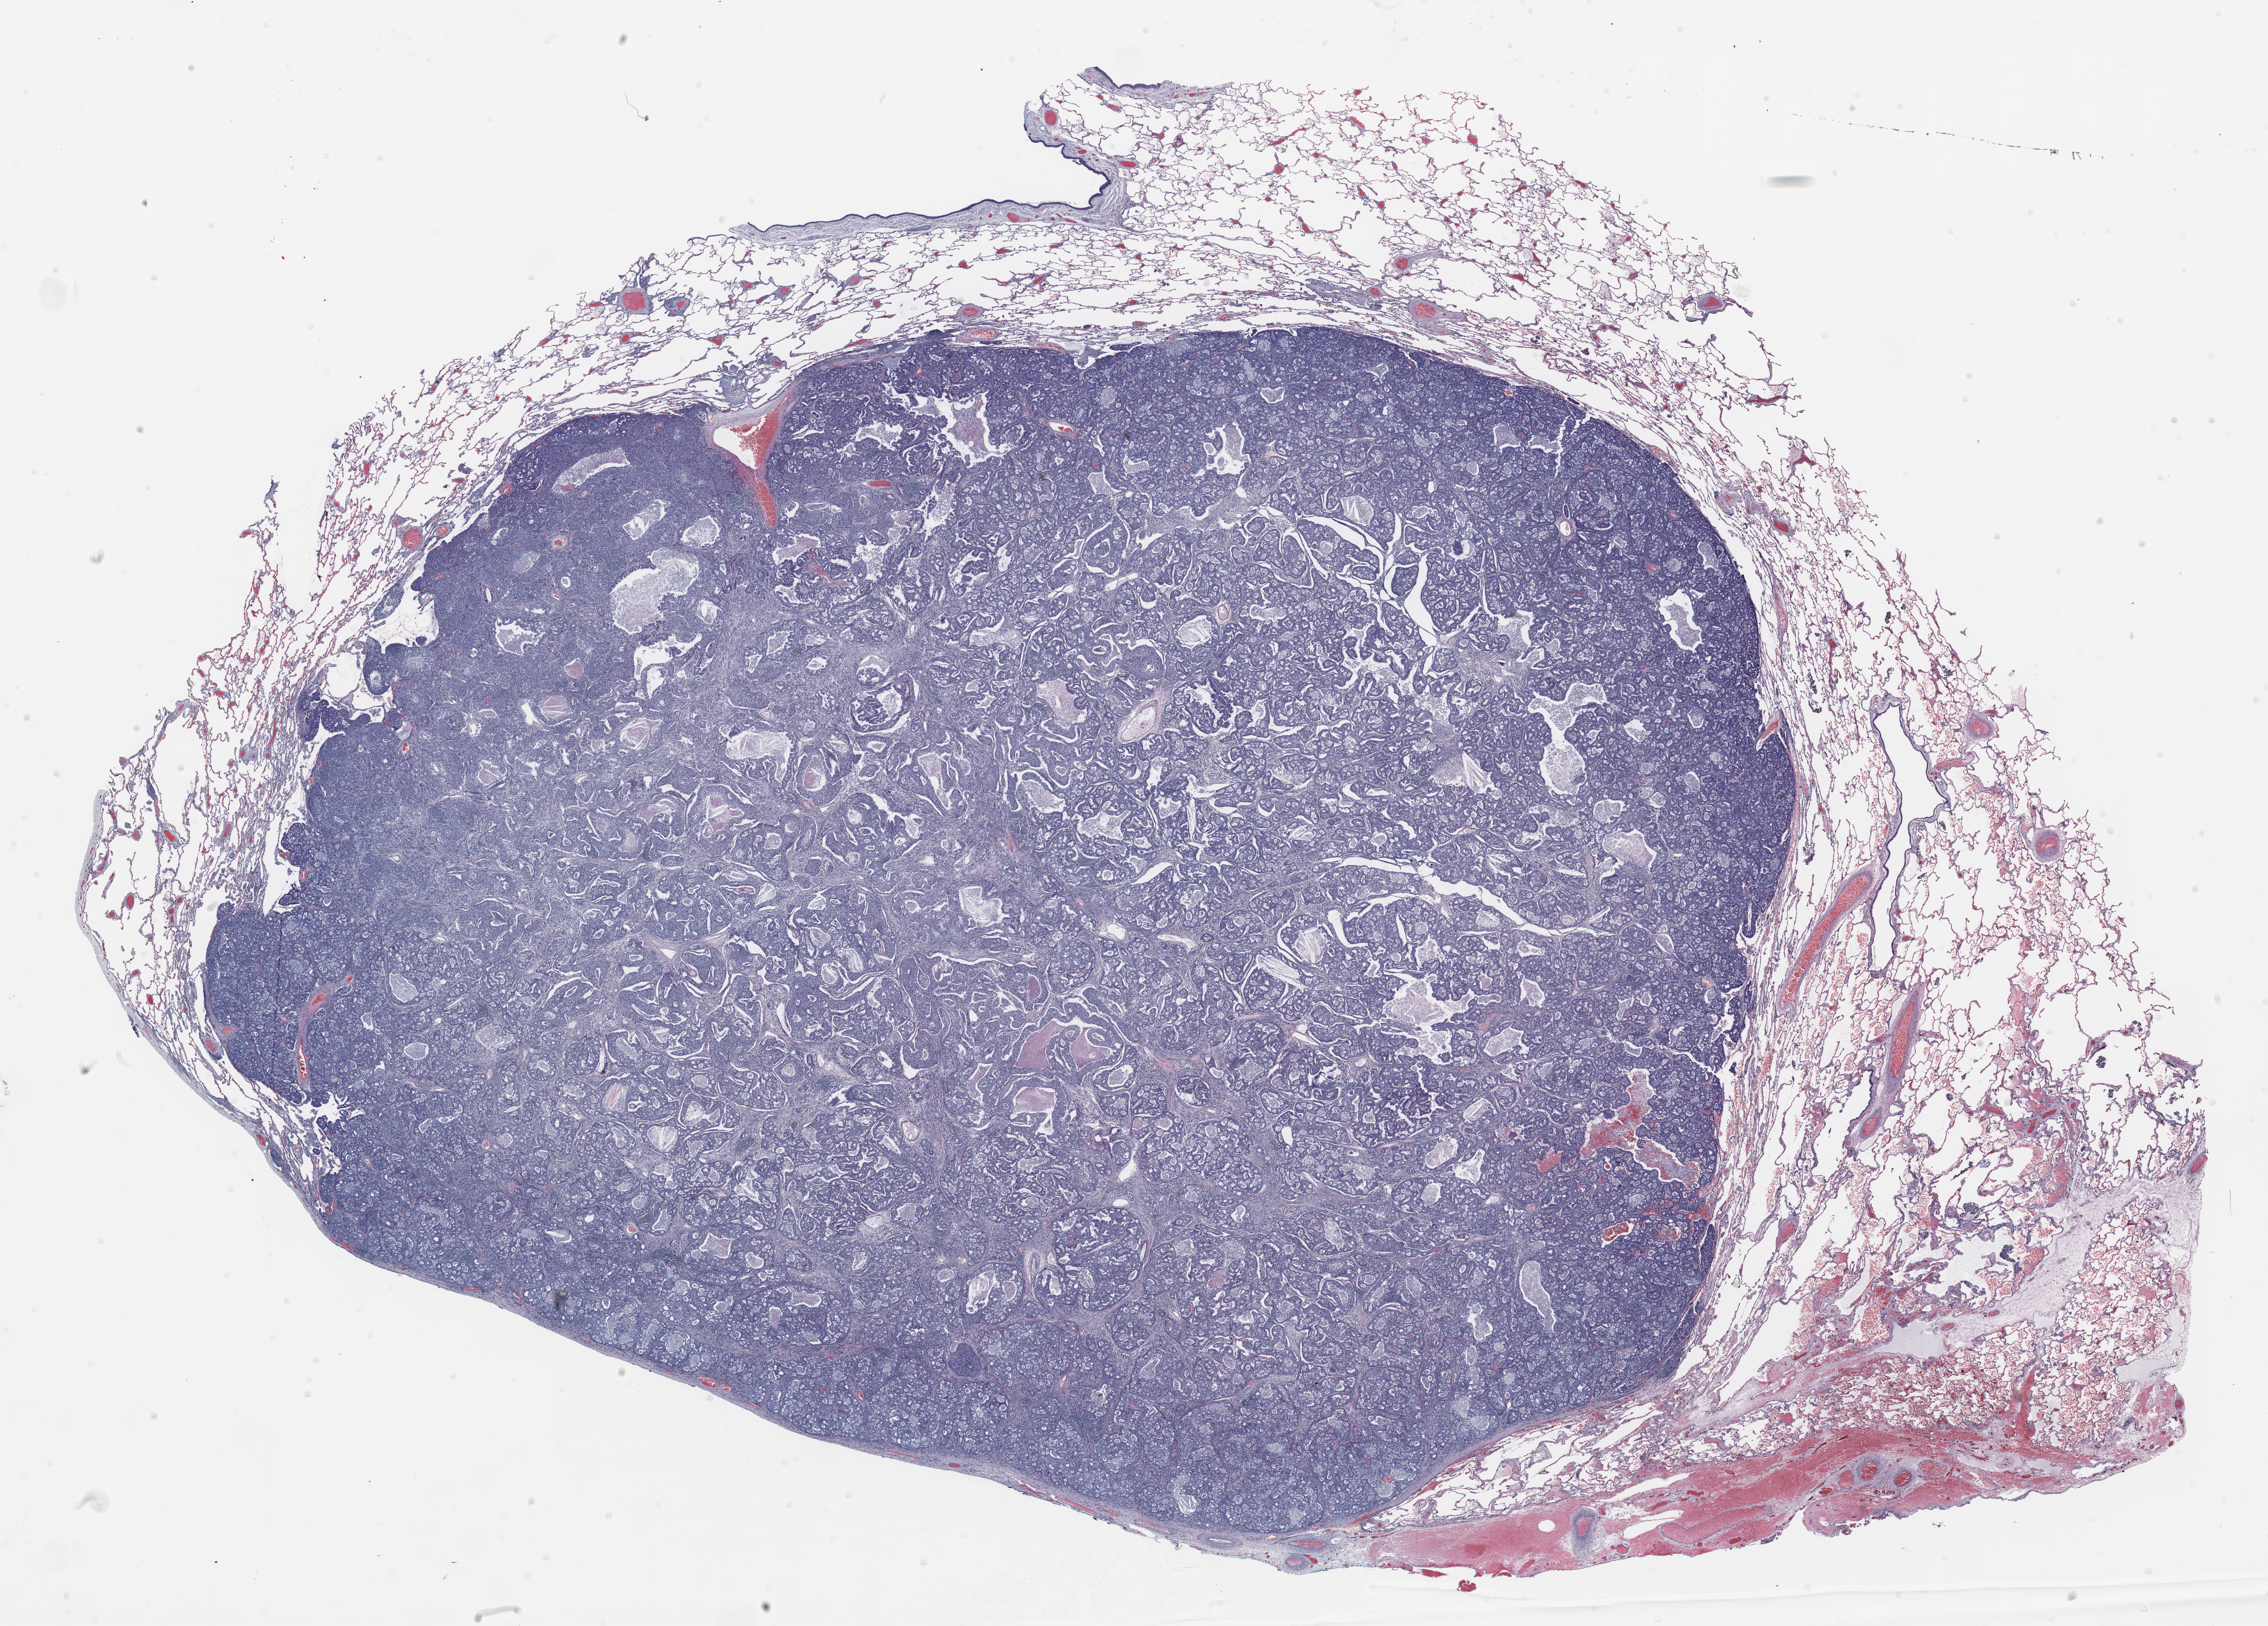
Hematoxylin and eosin (H&E) stained whole-slide image, low-resolution overview of the scanned area, about 31.0 x 22.2 mm (slide scanned at 20x), FFPE section, lung. Male, age 56 at enrolment. Former smoker at enrolment. Grade: moderately differentiated (G2).
* participant's lung-cancer diagnosis: Adenocarcinoma, NOS
* primary tumour location (clinical record): right middle lobe
* ICD-O-3 topography: middle lobe of lung (C34.2)
* stage (AJCC 6th edition): IA
* tumour size (pathology): 17 mm